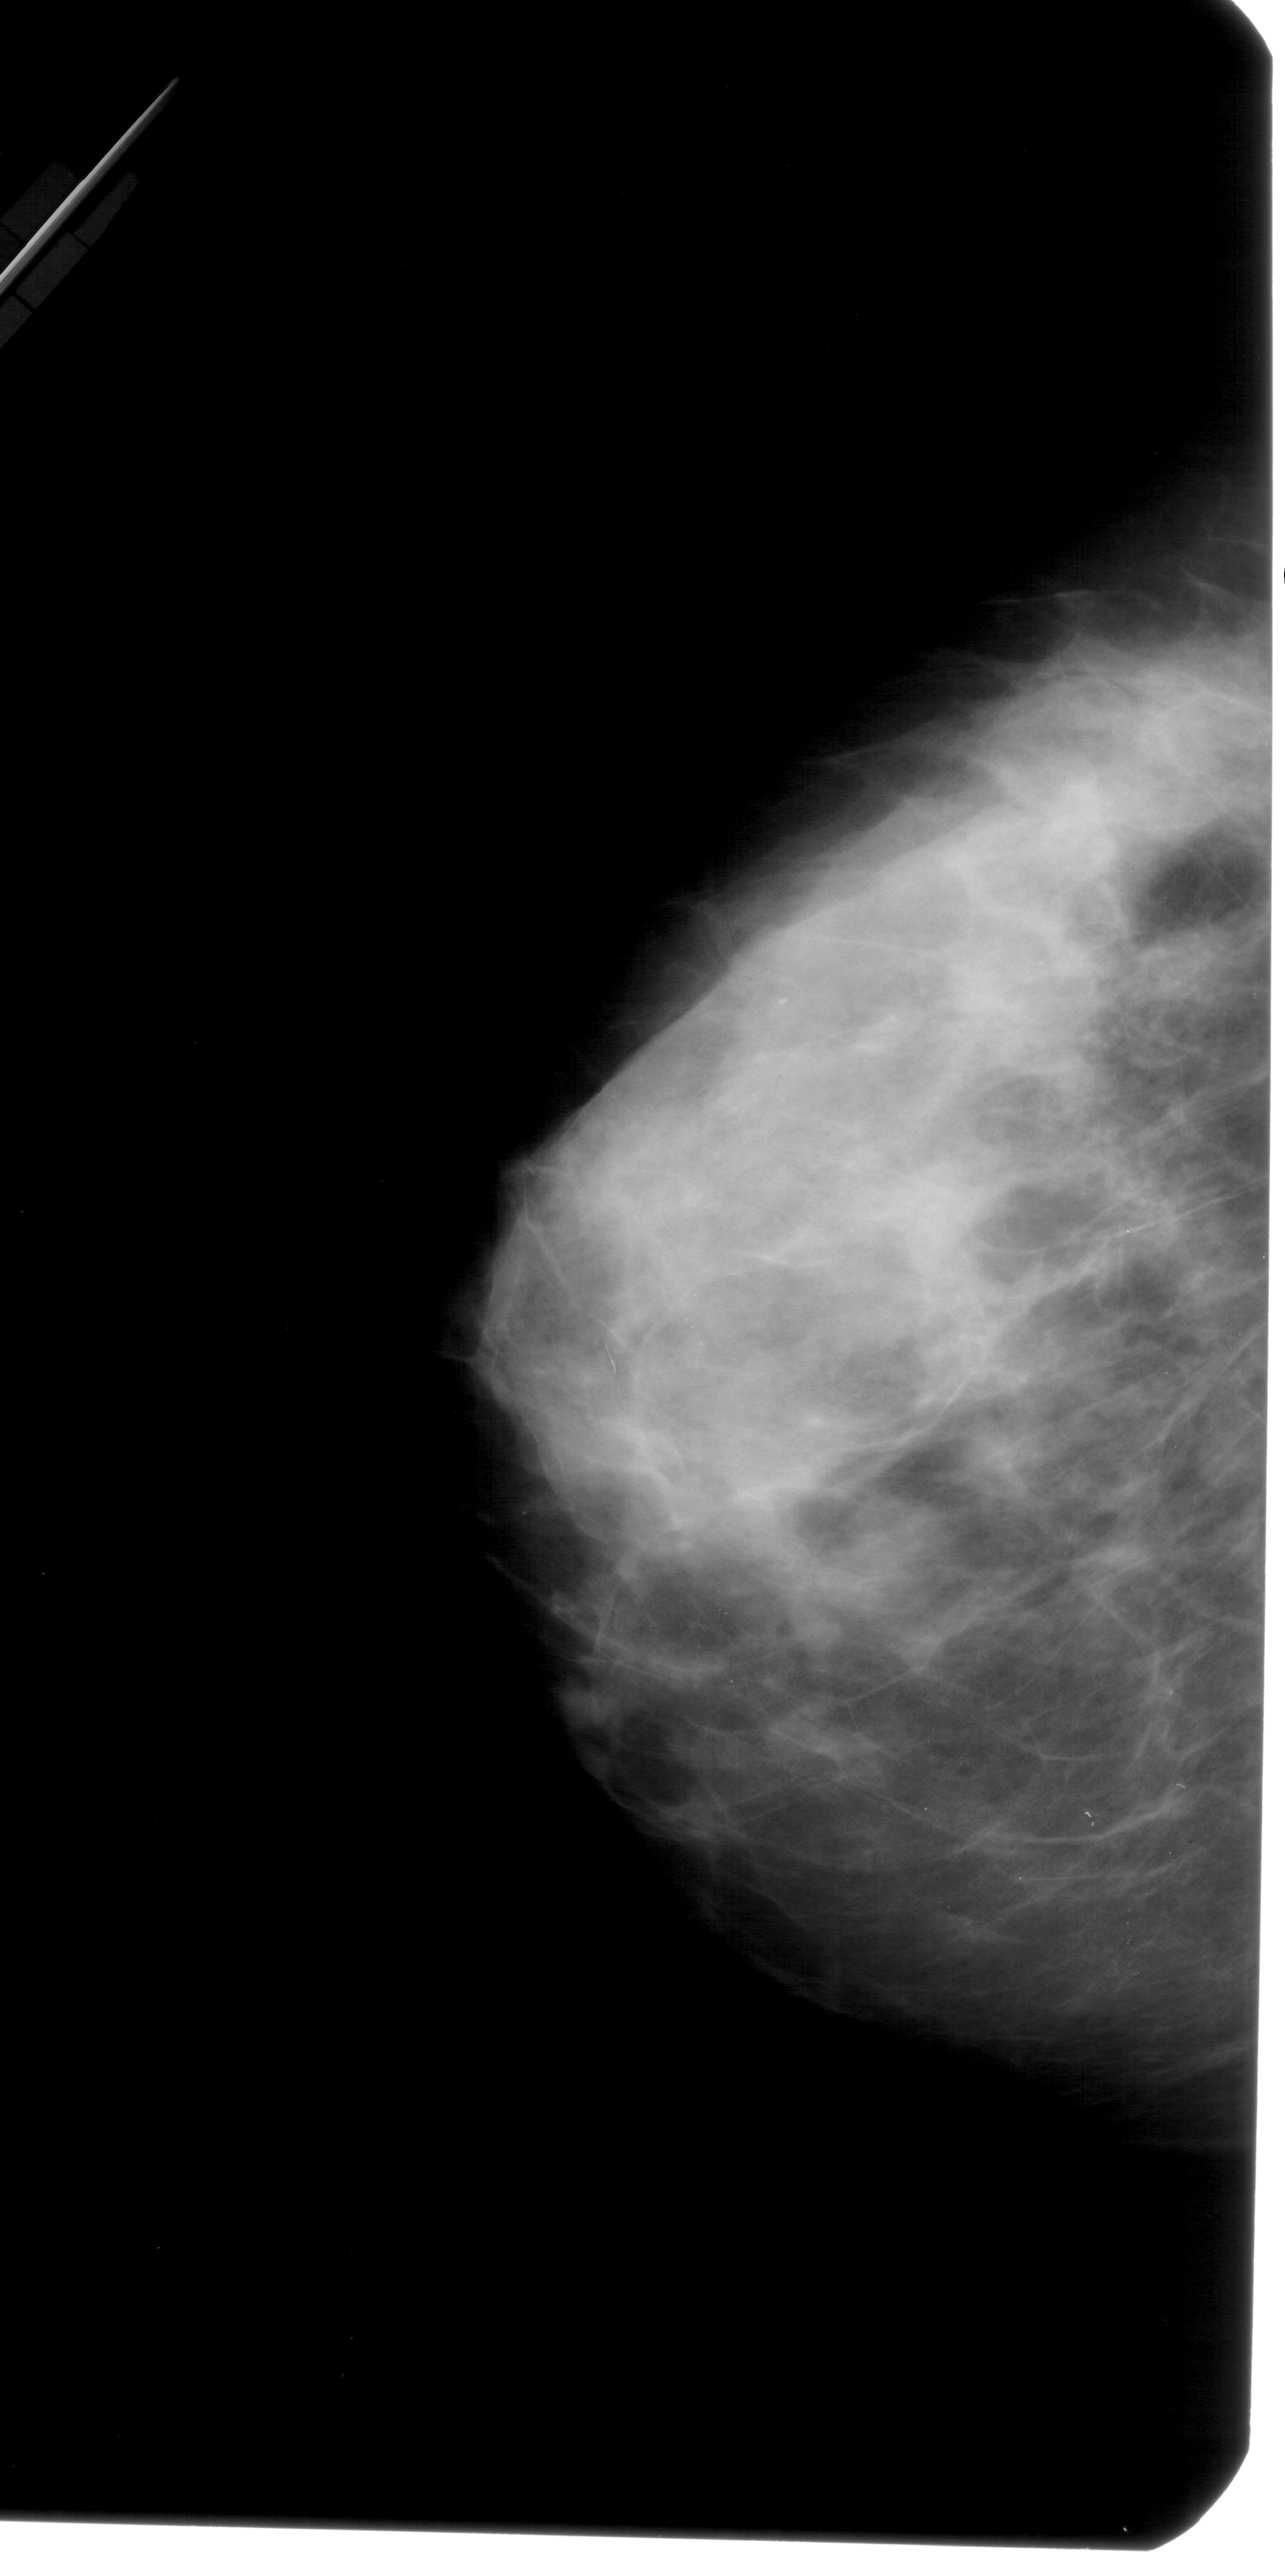
Mammogram (digitized film); left breast; craniocaudal (CC) view; 1285 × 2576 image matrix.
Expert-marked regions of interest on this image (one box per marked abnormality):
- calcifications, morphology punctate, distribution regional; BI-RADS assessment category 4; pathology (as recorded): malignant: bounding box [x1, y1, x2, y2] px = [596, 979, 1000, 1449]